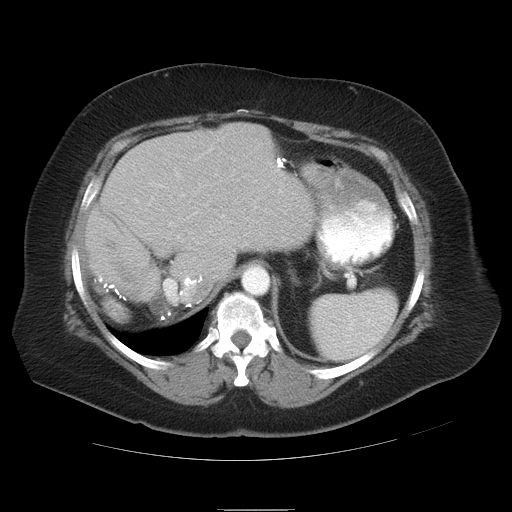
Contrast-enhanced abdominal CT, one axial slice. Slice 25 of 37 in the series (ordered by position). 120 kVp. Soft-tissue window (W 400 / L 40 HU). 512 × 512 image matrix. Female patient, age 68 years. Case-level facts recorded for this patient, not image findings: diagnosis: colorectal cancer liver metastases, imaged before liver resection; multiple liver metastases: no; largest metastasis: 2 cm; disease in both lobes: no.
Annotated regions visible in this slice (manually delineated by an expert):
- liver: bounding box [x1, y1, x2, y2] px = [86, 125, 315, 305]
- planned liver remnant (the part of the liver to remain after resection): [94, 124, 316, 305]
- portal vein (with intrahepatic branches): [149, 193, 222, 303]
- liver metastasis: [101, 238, 142, 289]